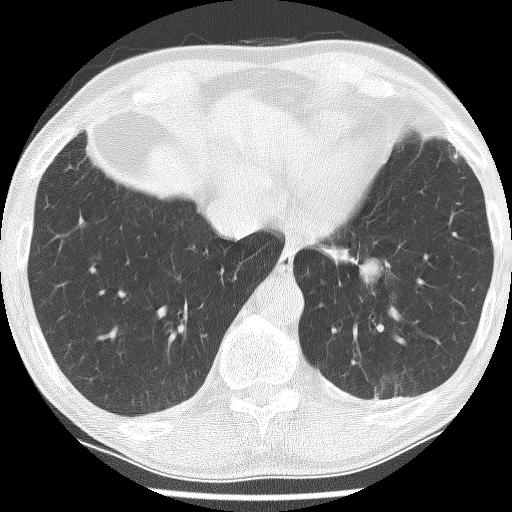
Low-dose screening chest CT, one axial slice; reconstruction kernel BONE; 120 kVp; lung window (W 1500 / L -600 HU); 512 × 512 image matrix.
Structures marked on this image (manually delineated by an expert):
- lesion 1 (tumor, lower lobe of left lung): bounding box [x1, y1, x2, y2] px = [359, 258, 385, 290]